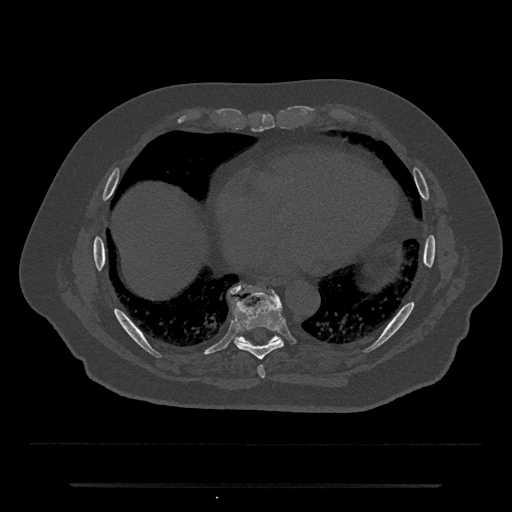
CT including the spine, one axial slice. Position 796 of 797 along the scan axis. Reconstruction kernel Br40s/3. Bone window (W 1800 / L 400 HU). 0.5 mm slice thickness. 512 × 512 image matrix, field of view 434 × 434 mm. Patient: male, 80 years. Case-level facts recorded for this patient, not image findings: primary cancer: prostate; vertebrae with lytic lesions (as recorded): L1, T11.
Structures marked on this image (semi-automatic segmentation, software-assisted and operator-edited):
- T8 vertebra: bounding box (x1, y1, x2, y2) in pixels: (233, 296, 284, 360)
- T9 vertebra: (229, 285, 281, 347)